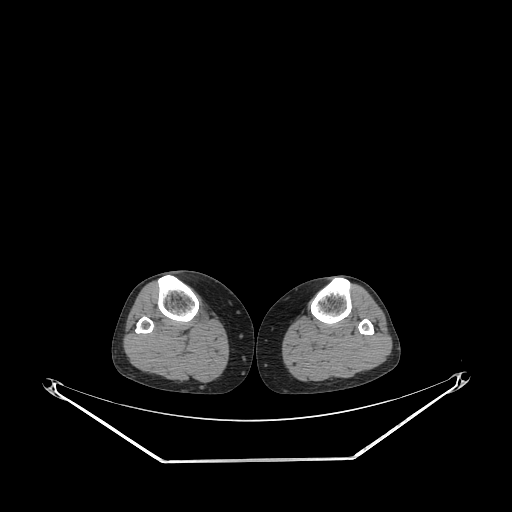
CT of an extremity soft-tissue mass (from a PET/CT study), one axial slice. Position 157 of 267 along the scan axis. Soft-tissue window (W 400 / L 40 HU). 512 × 512 image matrix, field of view 500 × 500 mm. Female patient. From the clinical record (not read from this slice): histological type: undifferentiated – high grade; grade: high; site of the primary tumour: right thigh.
Structures marked on this image (expert contour drawn on MRI and transferred to this co-registered scan by the dataset authors):
- gross tumour volume (mass): bounding box <198,304,211,325> (left, top, right, bottom; pixels)